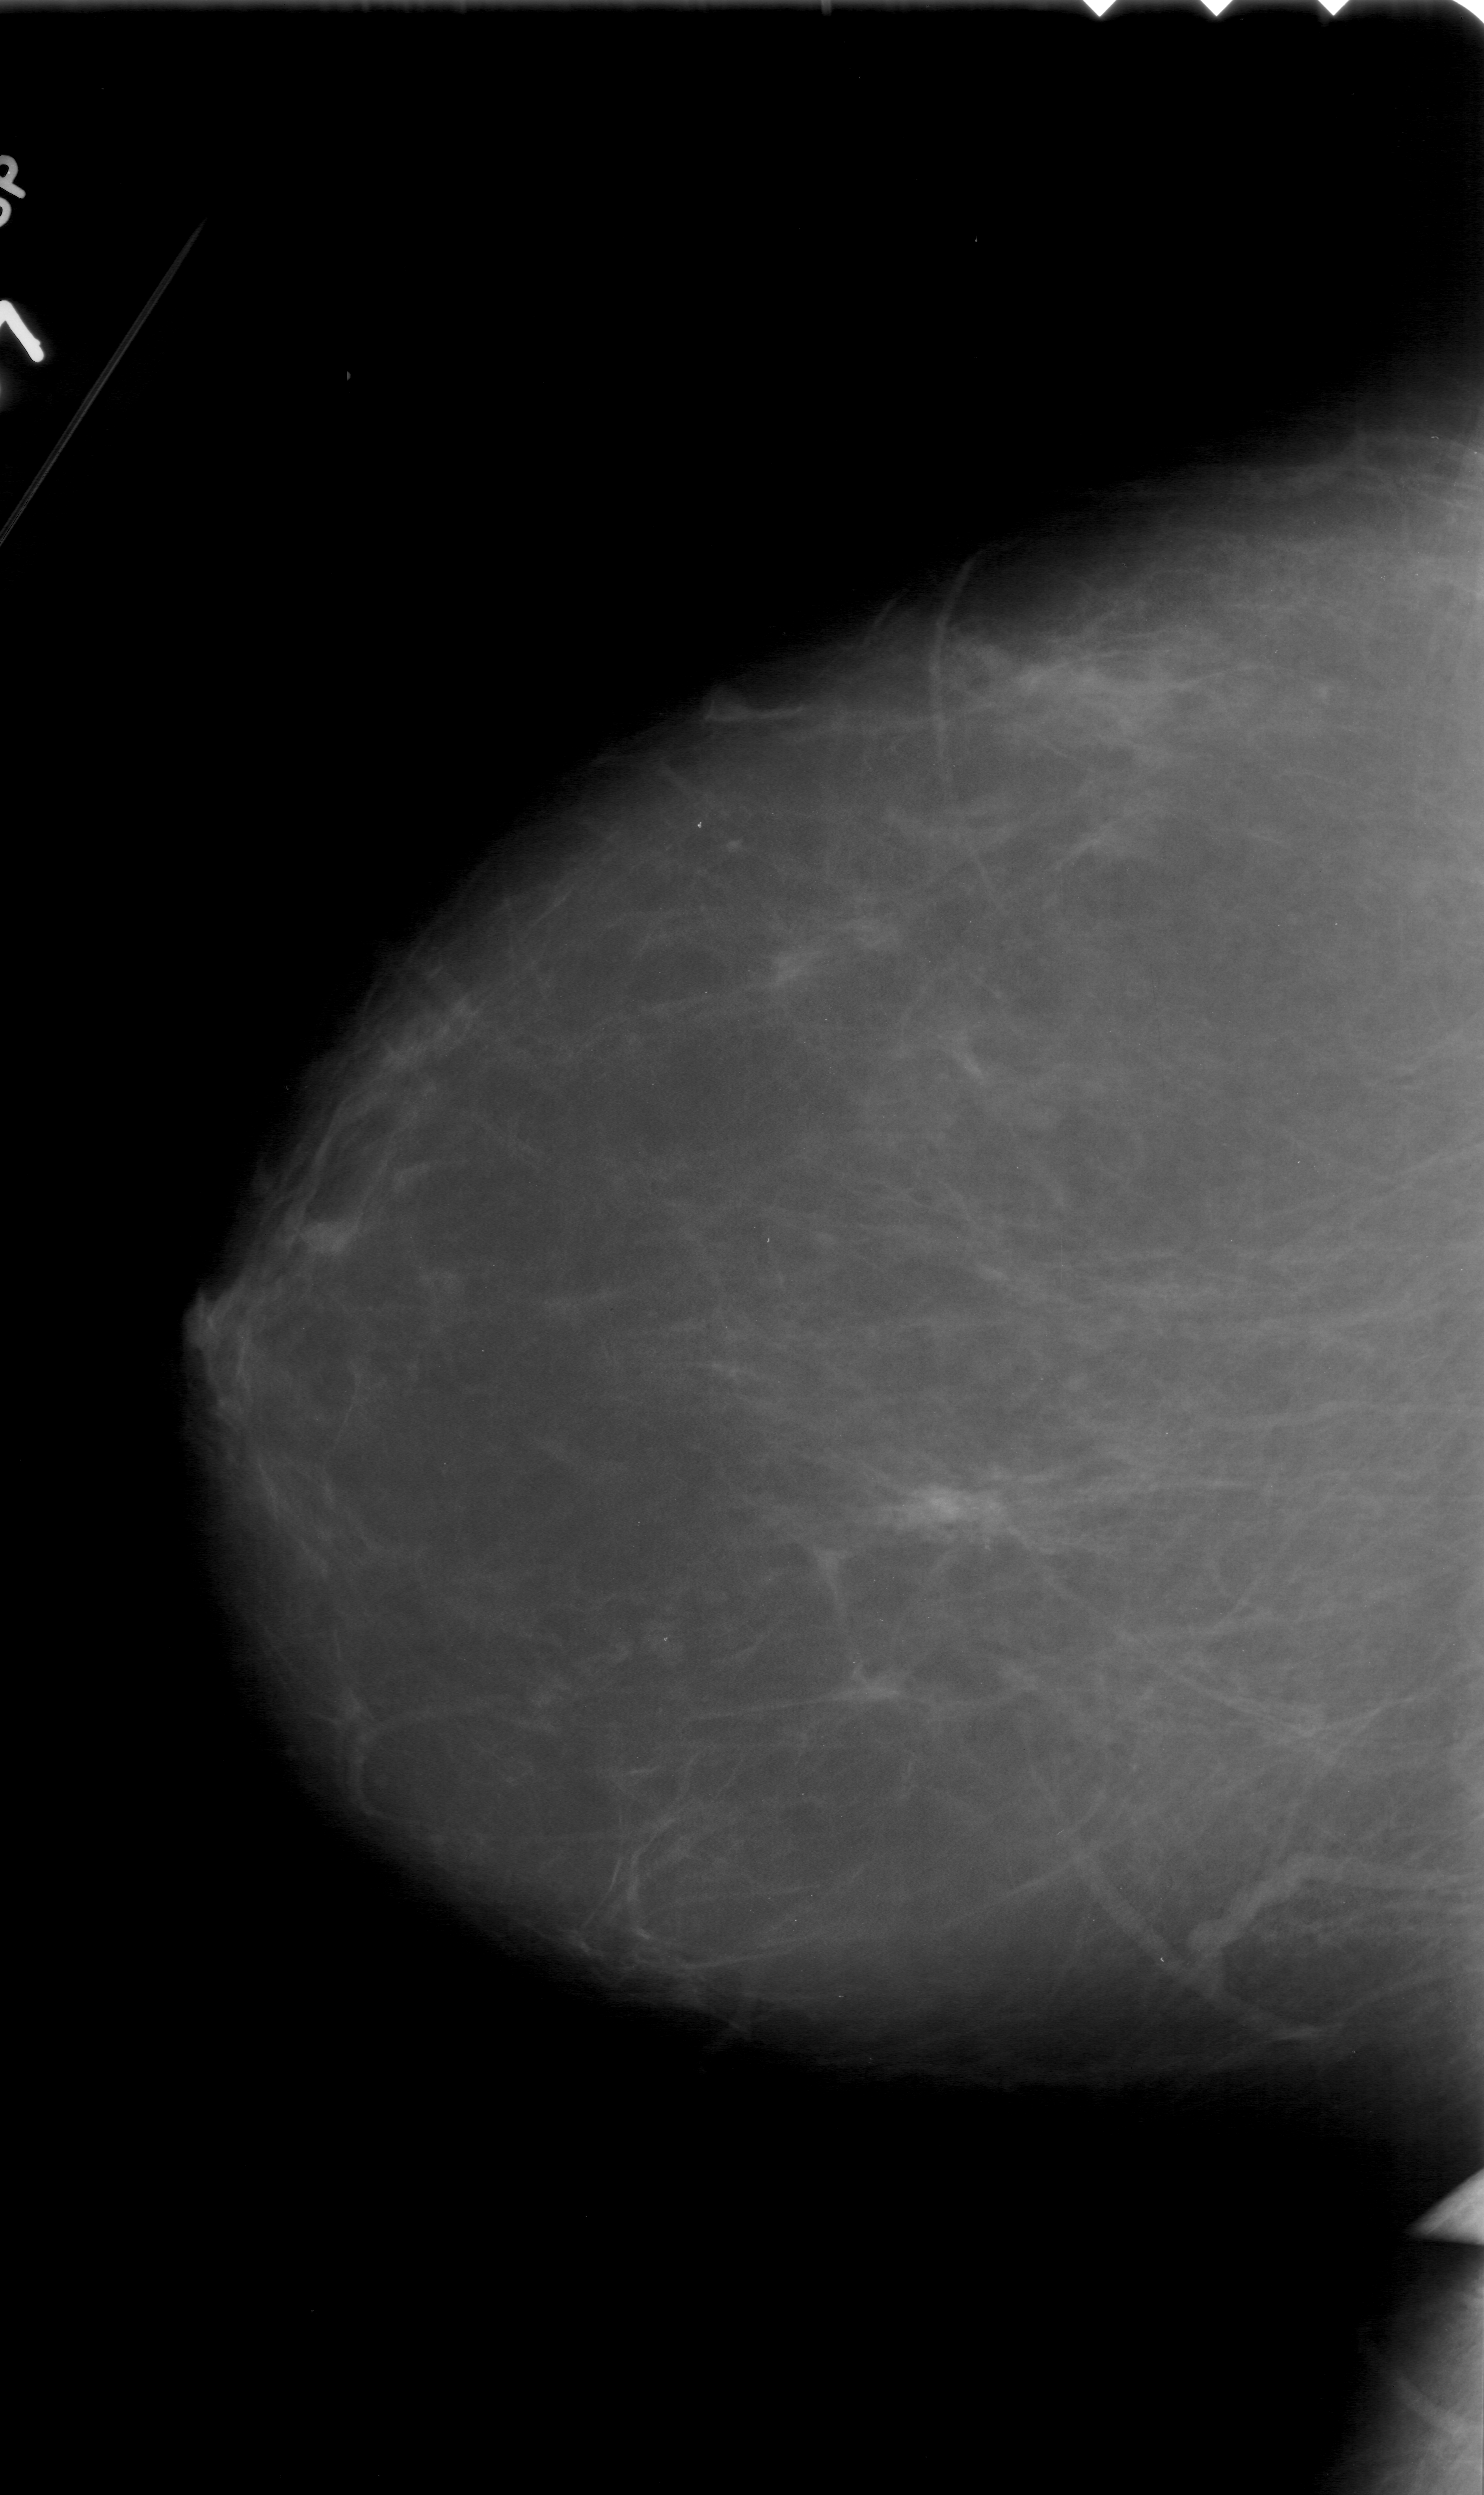
Mammogram (digitized film). Left breast. CC view. BI-RADS breast density category 2 (scale 1–4). 1484 × 2495 image matrix.
Expert-marked regions of interest on this film, with their recorded descriptors:
- calcifications, morphology pleomorphic, distribution clustered; BI-RADS assessment category 4; subtlety rating 1 on a 1 (subtle) to 5 (obvious) scale; pathology (as recorded): malignant: bounding box (x1, y1, x2, y2) in pixels: (894, 1467, 1031, 1557)